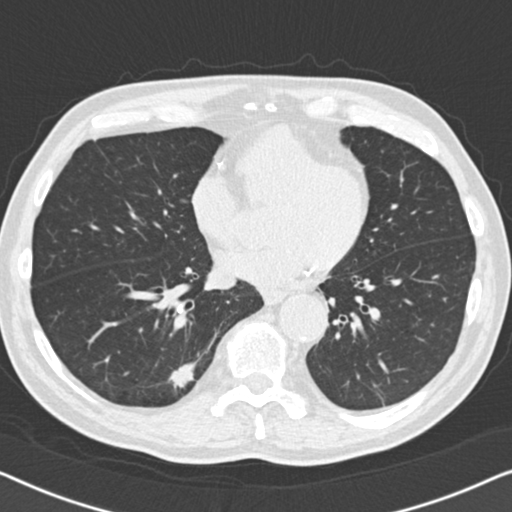
Low-dose screening chest CT, one axial slice; position 56 of 164 along the scan axis; lung window (W 1500 / L -600 HU); 2 mm slice thickness; 512 × 512 image matrix.
Outlined on this slice (outlined manually by an expert reader):
- lesion 1 (tumor, lower lobe of right lung): bounding box <168,361,197,390> (left, top, right, bottom; pixels)